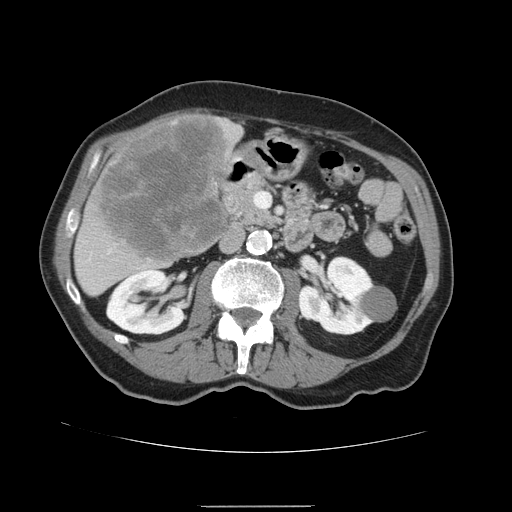
Contrast-enhanced abdominal CT, one axial slice. Slice 61 of 168 in the series (ordered by position). Intravenous contrast given. Soft-tissue window (W 400 / L 40 HU). 2.5 mm slice thickness. 512 × 512 image matrix, field of view 386 × 386 mm. Male patient, age 74 years. Case-level facts recorded for this patient, not image findings: diagnosis: colorectal cancer liver metastases, imaged before liver resection; multiple liver metastases: no; largest metastasis: 14.5 cm; disease in both lobes: yes.
Outlined on this slice (expert manual segmentation):
- liver: bounding box (x1, y1, x2, y2) in pixels: (74, 113, 244, 297)
- liver metastasis: (95, 117, 229, 264)